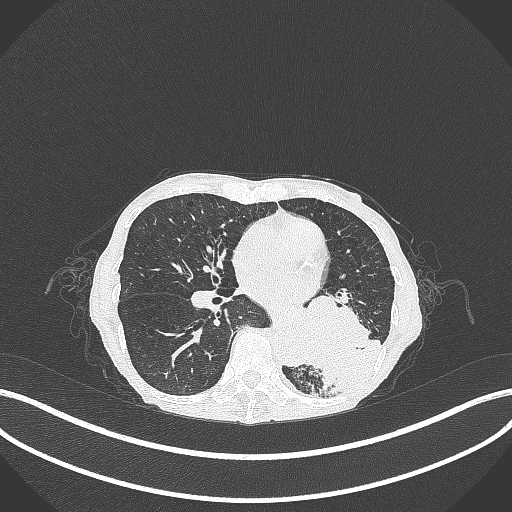
Chest CT, one axial slice; slice 123 of 347 in the series (ordered by position); reconstruction kernel B70f; lung window (W 1500 / L -600 HU); 1 mm slice thickness; 512 × 512 image matrix. Female patient, age 70 years. Case-level facts recorded for this patient, not image findings: clinical TNM (as recorded): T3 N0 M0.
Structures marked on this image (bounding box drawn by a radiologist):
- lung tumour (recorded histology: small cell carcinoma): bounding box (x1, y1, x2, y2) in pixels: (286, 295, 380, 386)